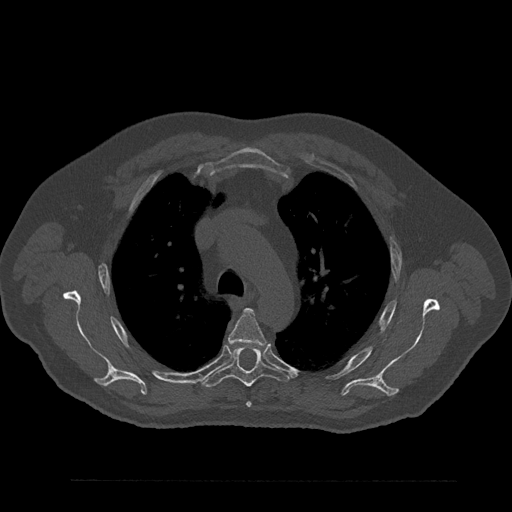
CT including the spine, one axial slice; position 618 of 797 along the scan axis; reconstruction kernel Br40s/3; 120 kVp; bone window (W 1800 / L 400 HU); 0.5 mm slice thickness; 512 × 512 image matrix, field of view 430 × 430 mm. Male patient, age 61 years. Case-level facts recorded for this patient, not image findings: primary cancer: prostate.
Outlined on this slice (semi-automatically segmented with operator editing):
- T4 vertebra: bounding box [x1, y1, x2, y2] px = [228, 309, 266, 408]
- T5 vertebra: [202, 348, 289, 387]